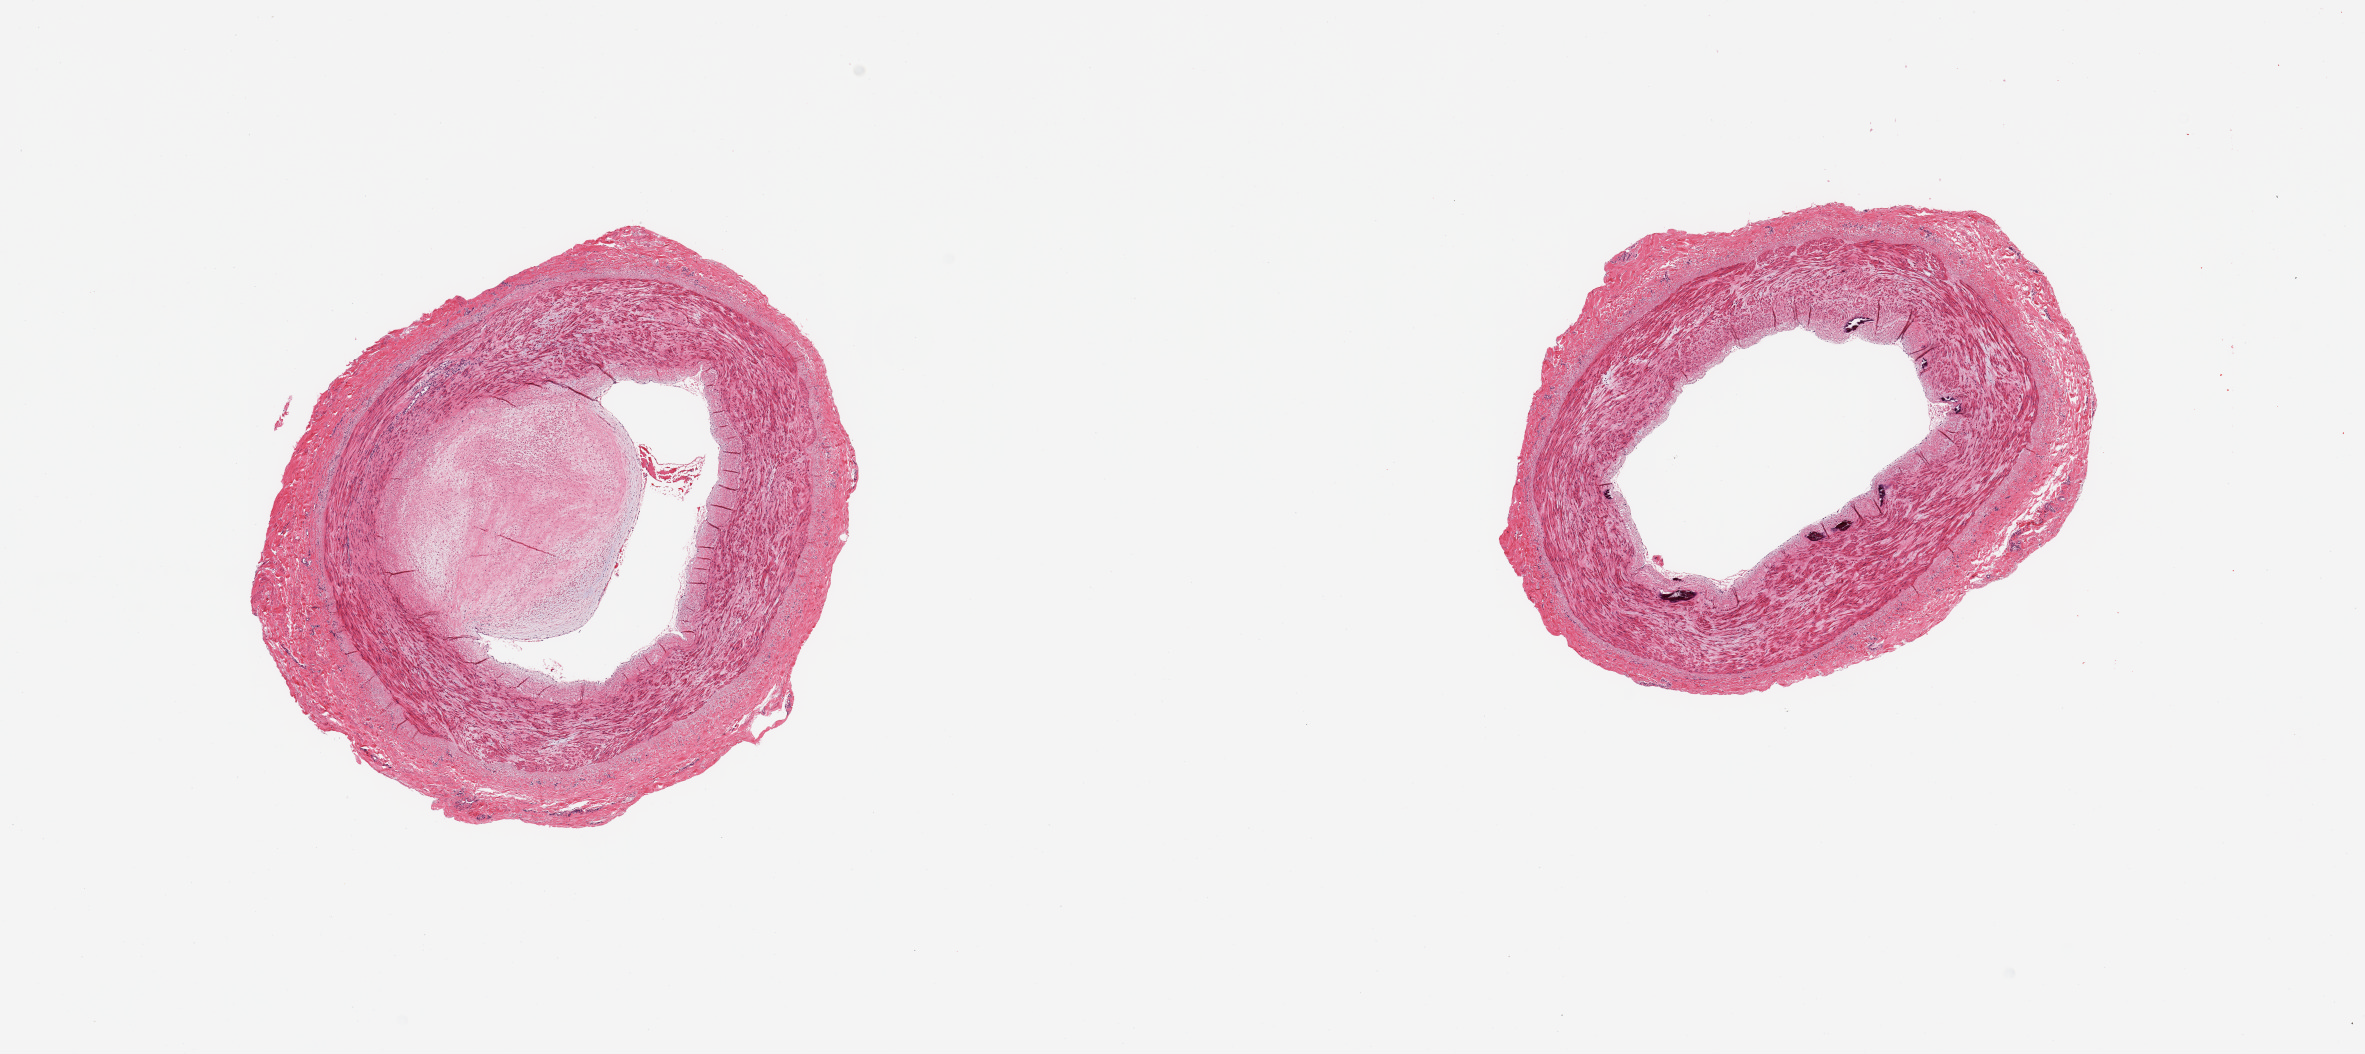
H&E whole-slide image — a low-resolution overview of the entire scanned area, about 18.7 x 8.3 mm; PAXgene-fixed paraffin-embedded (PFPE) section; section of tibial artery (target tissue); donor tissue sample. Donor sex: female.
Review note (as recorded): 2 pieces, minimal adherent fat, subtotally occlusive atherosis, focal calcifications noted more c/w Monckeberg's.